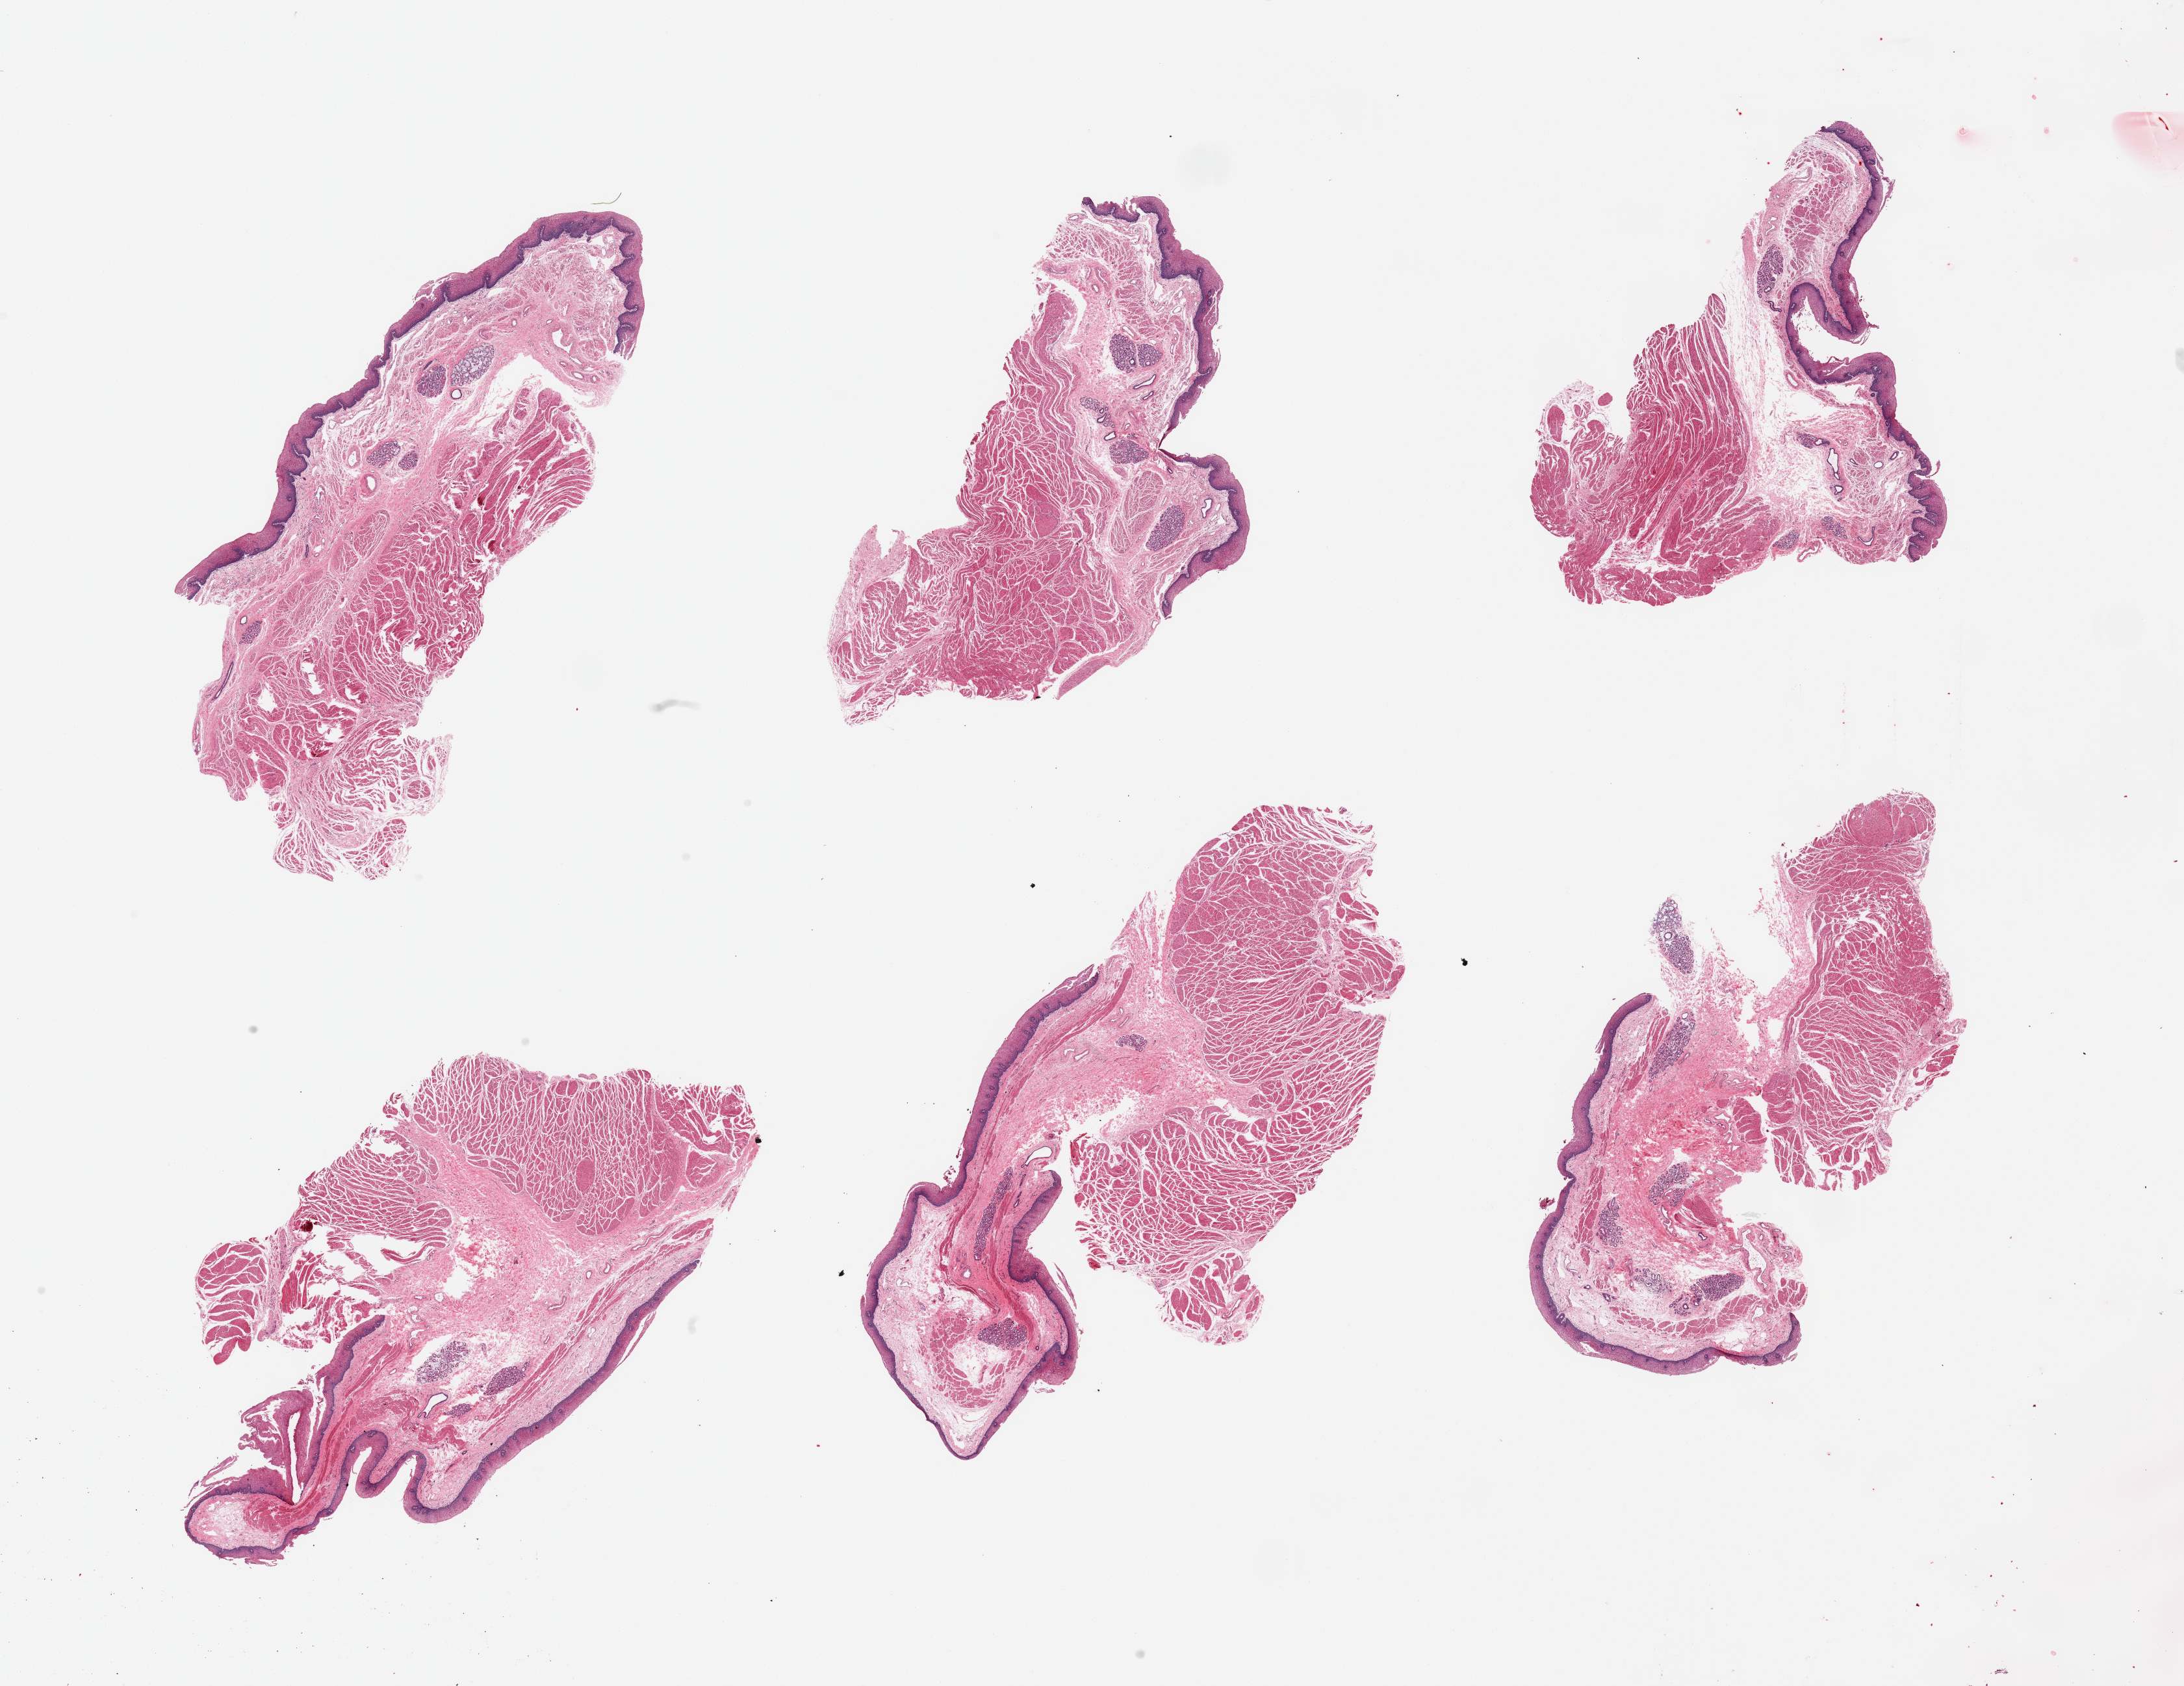
Whole-slide image, haematoxylin and eosin stain, brightfield — whole scanned area (about 26.6 x 20.5 mm) shown as a low-resolution overview. PAXgene-fixed, paraffin-embedded tissue. Sampled site (target tissue): esophageal mucous membrane. Tissue donor sample. Donor sex: female.
Review note (as recorded): 6 pieces; all include significant component of muscularis (not target).